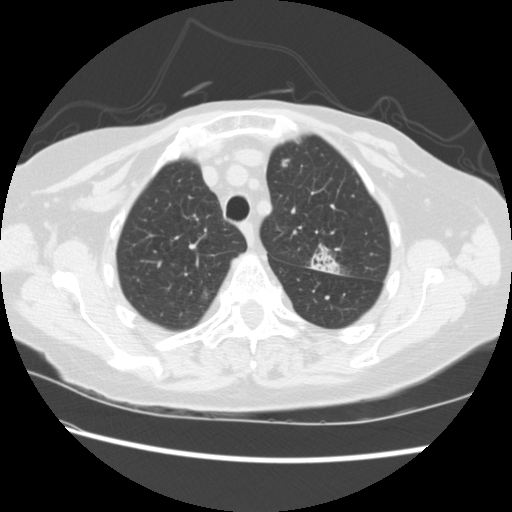
Low-dose screening chest CT, one axial slice; slice 172 of 224 in the series (ordered by position); lung window (W 1500 / L -600 HU); 2.5 mm slice thickness; 512 × 512 image matrix, field of view 340 × 340 mm.
Outlined on this slice (expert manual segmentation):
- lesion 1 (tumor, upper lobe of left lung): bounding box [x1, y1, x2, y2] px = [310, 245, 340, 274]